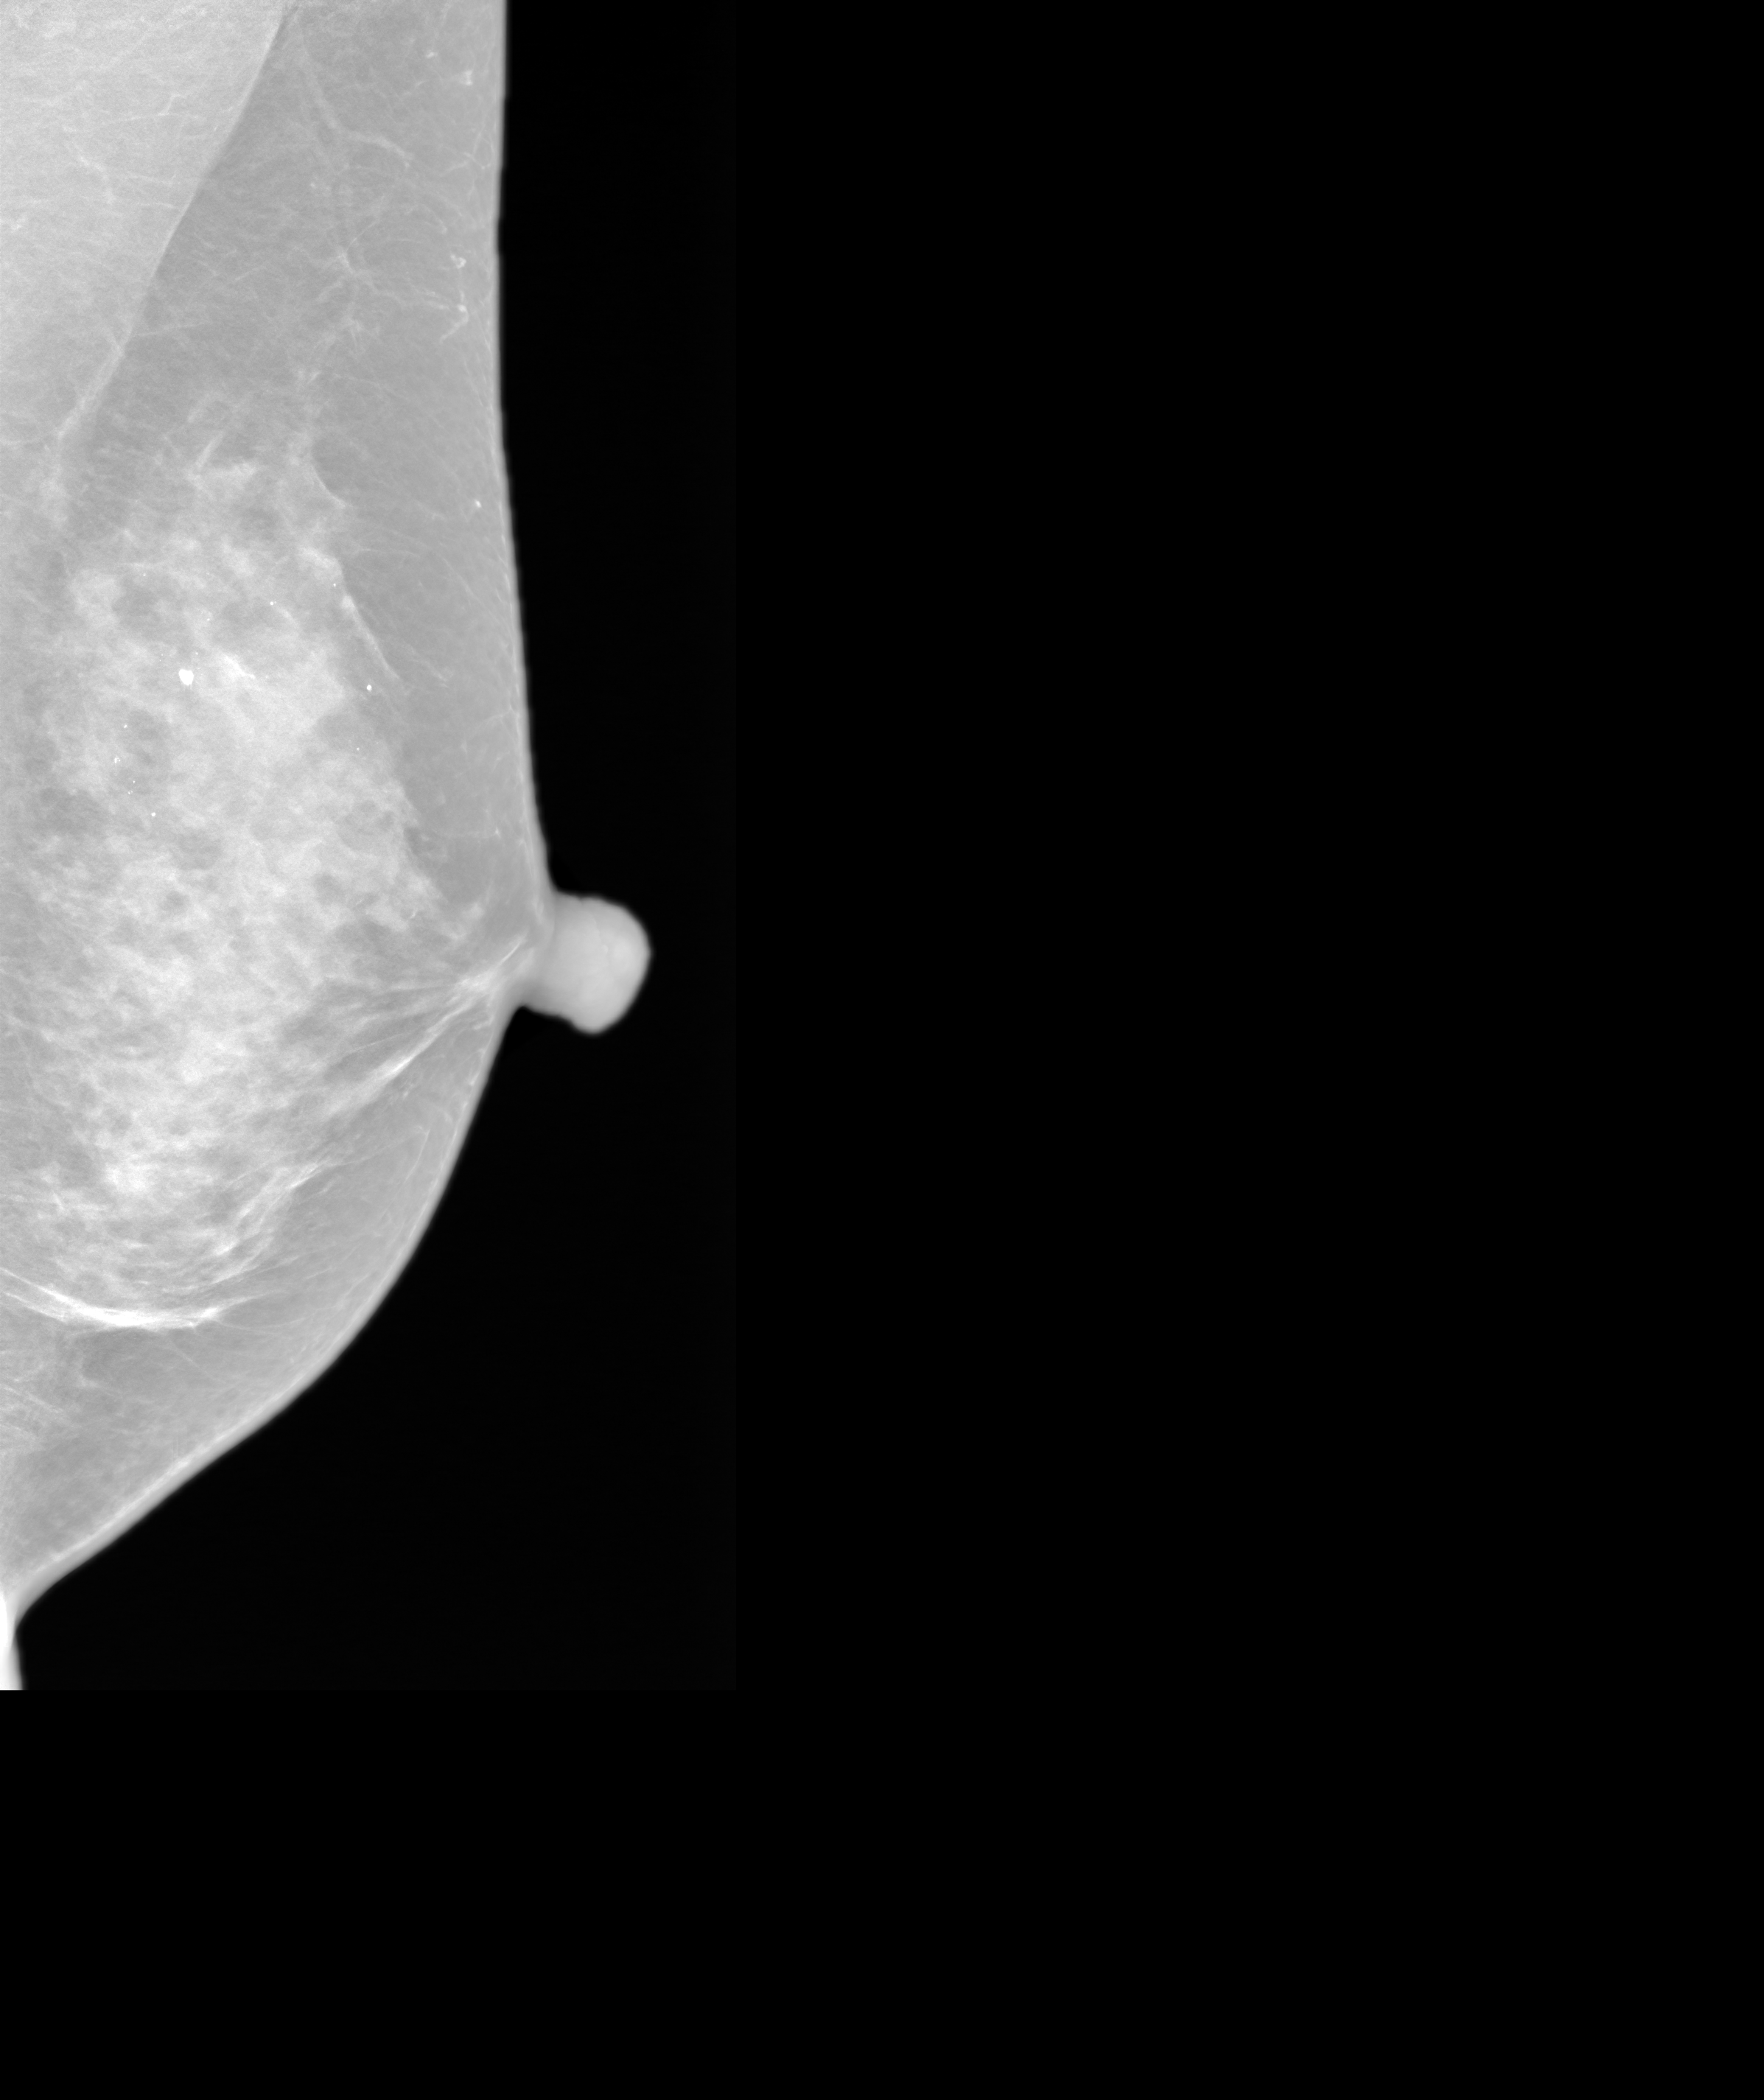
Screening examination.
Image type: synthesized 2-D view from tomosynthesis. Breast: left. Projection: mediolateral oblique (MLO) view.